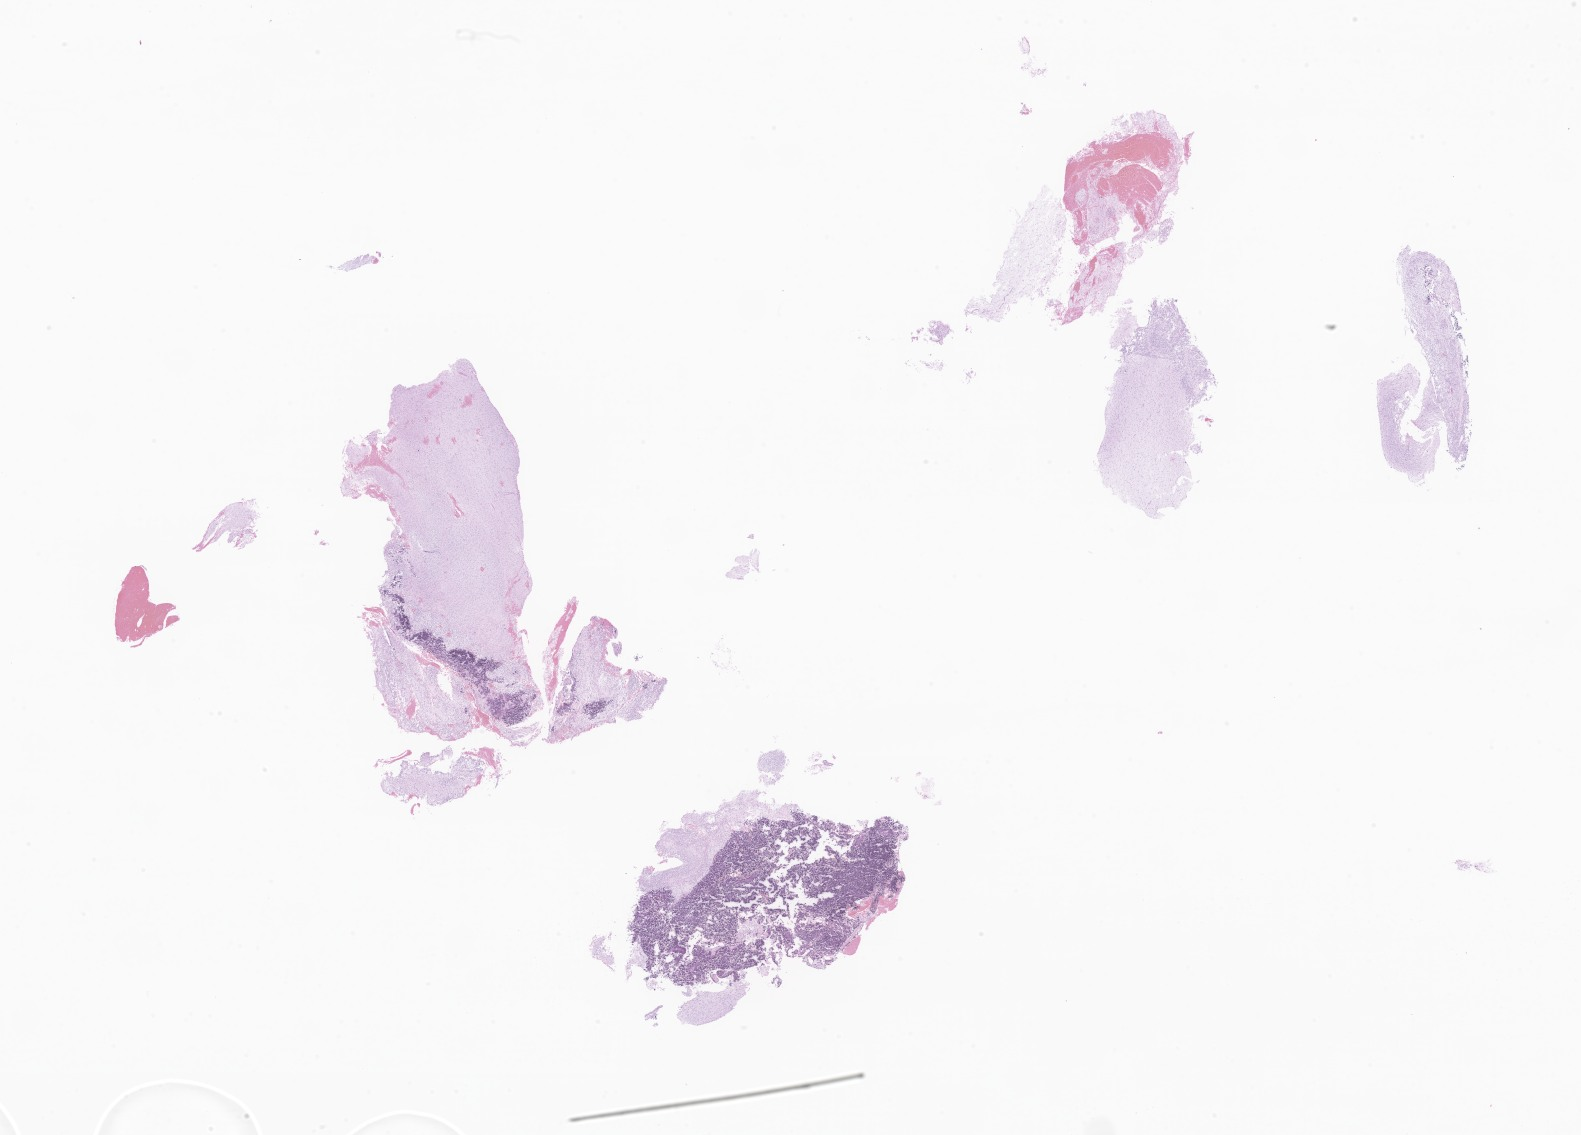
H&E whole-slide image of tumor tissue from the brain — shown as a low-resolution overview of the whole scanned area (about 26.7 x 19.1 mm), formalin-fixed, paraffin-embedded (FFPE) tissue. Patient female; age 57 days.
Diagnosis: Glioma, malignant.